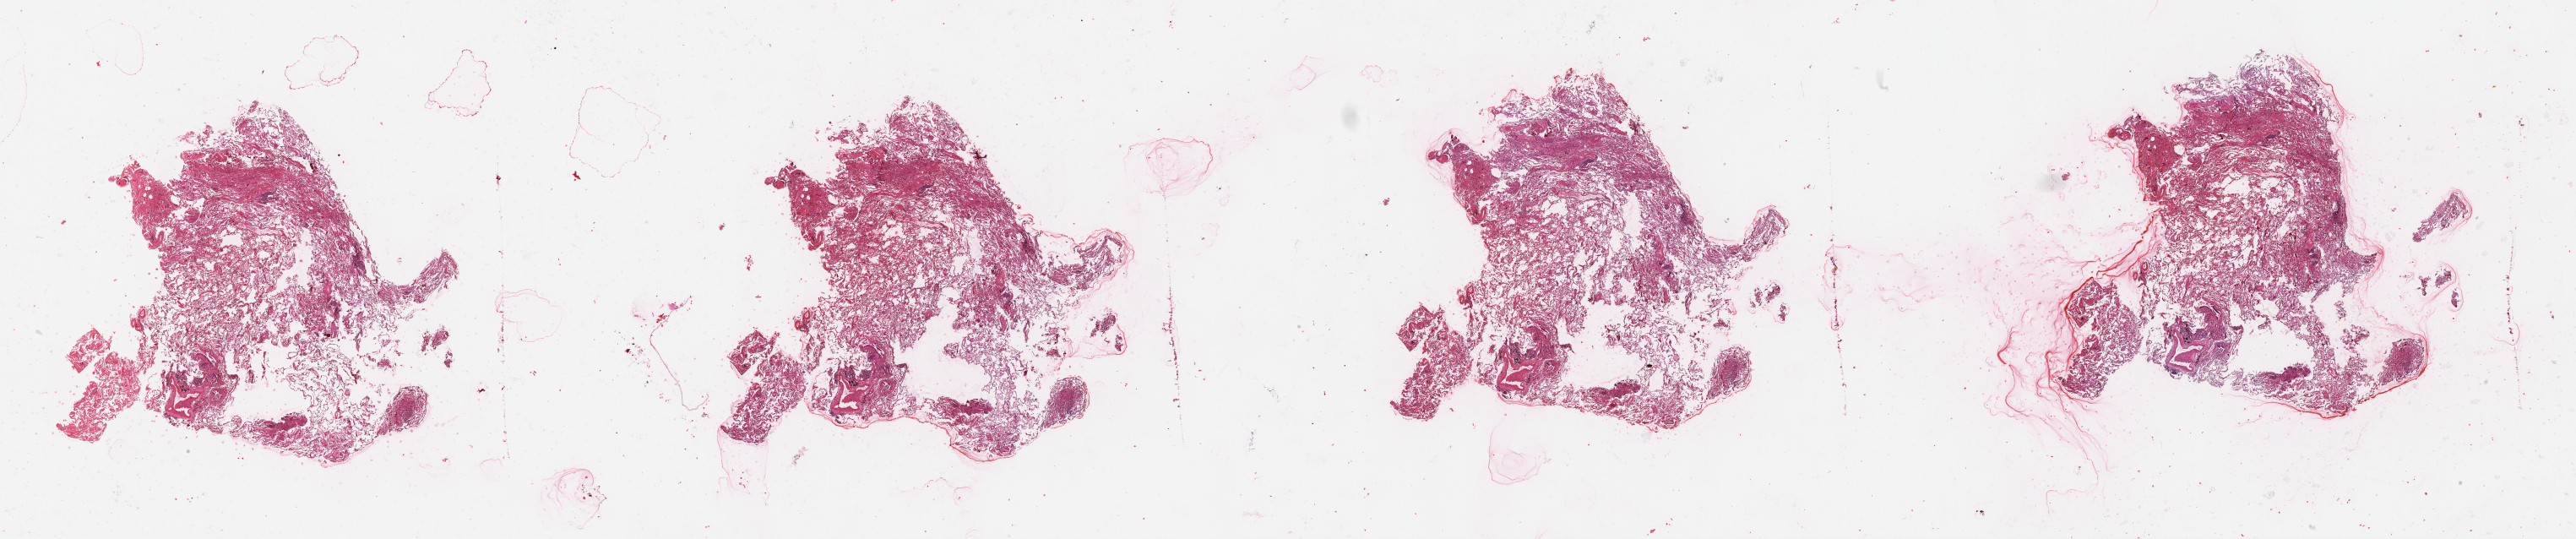
H&E-stained whole-slide image — a low-resolution overview of the entire scanned area, about 49.1 x 10.3 mm, lung, tissue type not recorded.
Patient diagnosis (cohort enrolment): squamous cell carcinoma (lung).